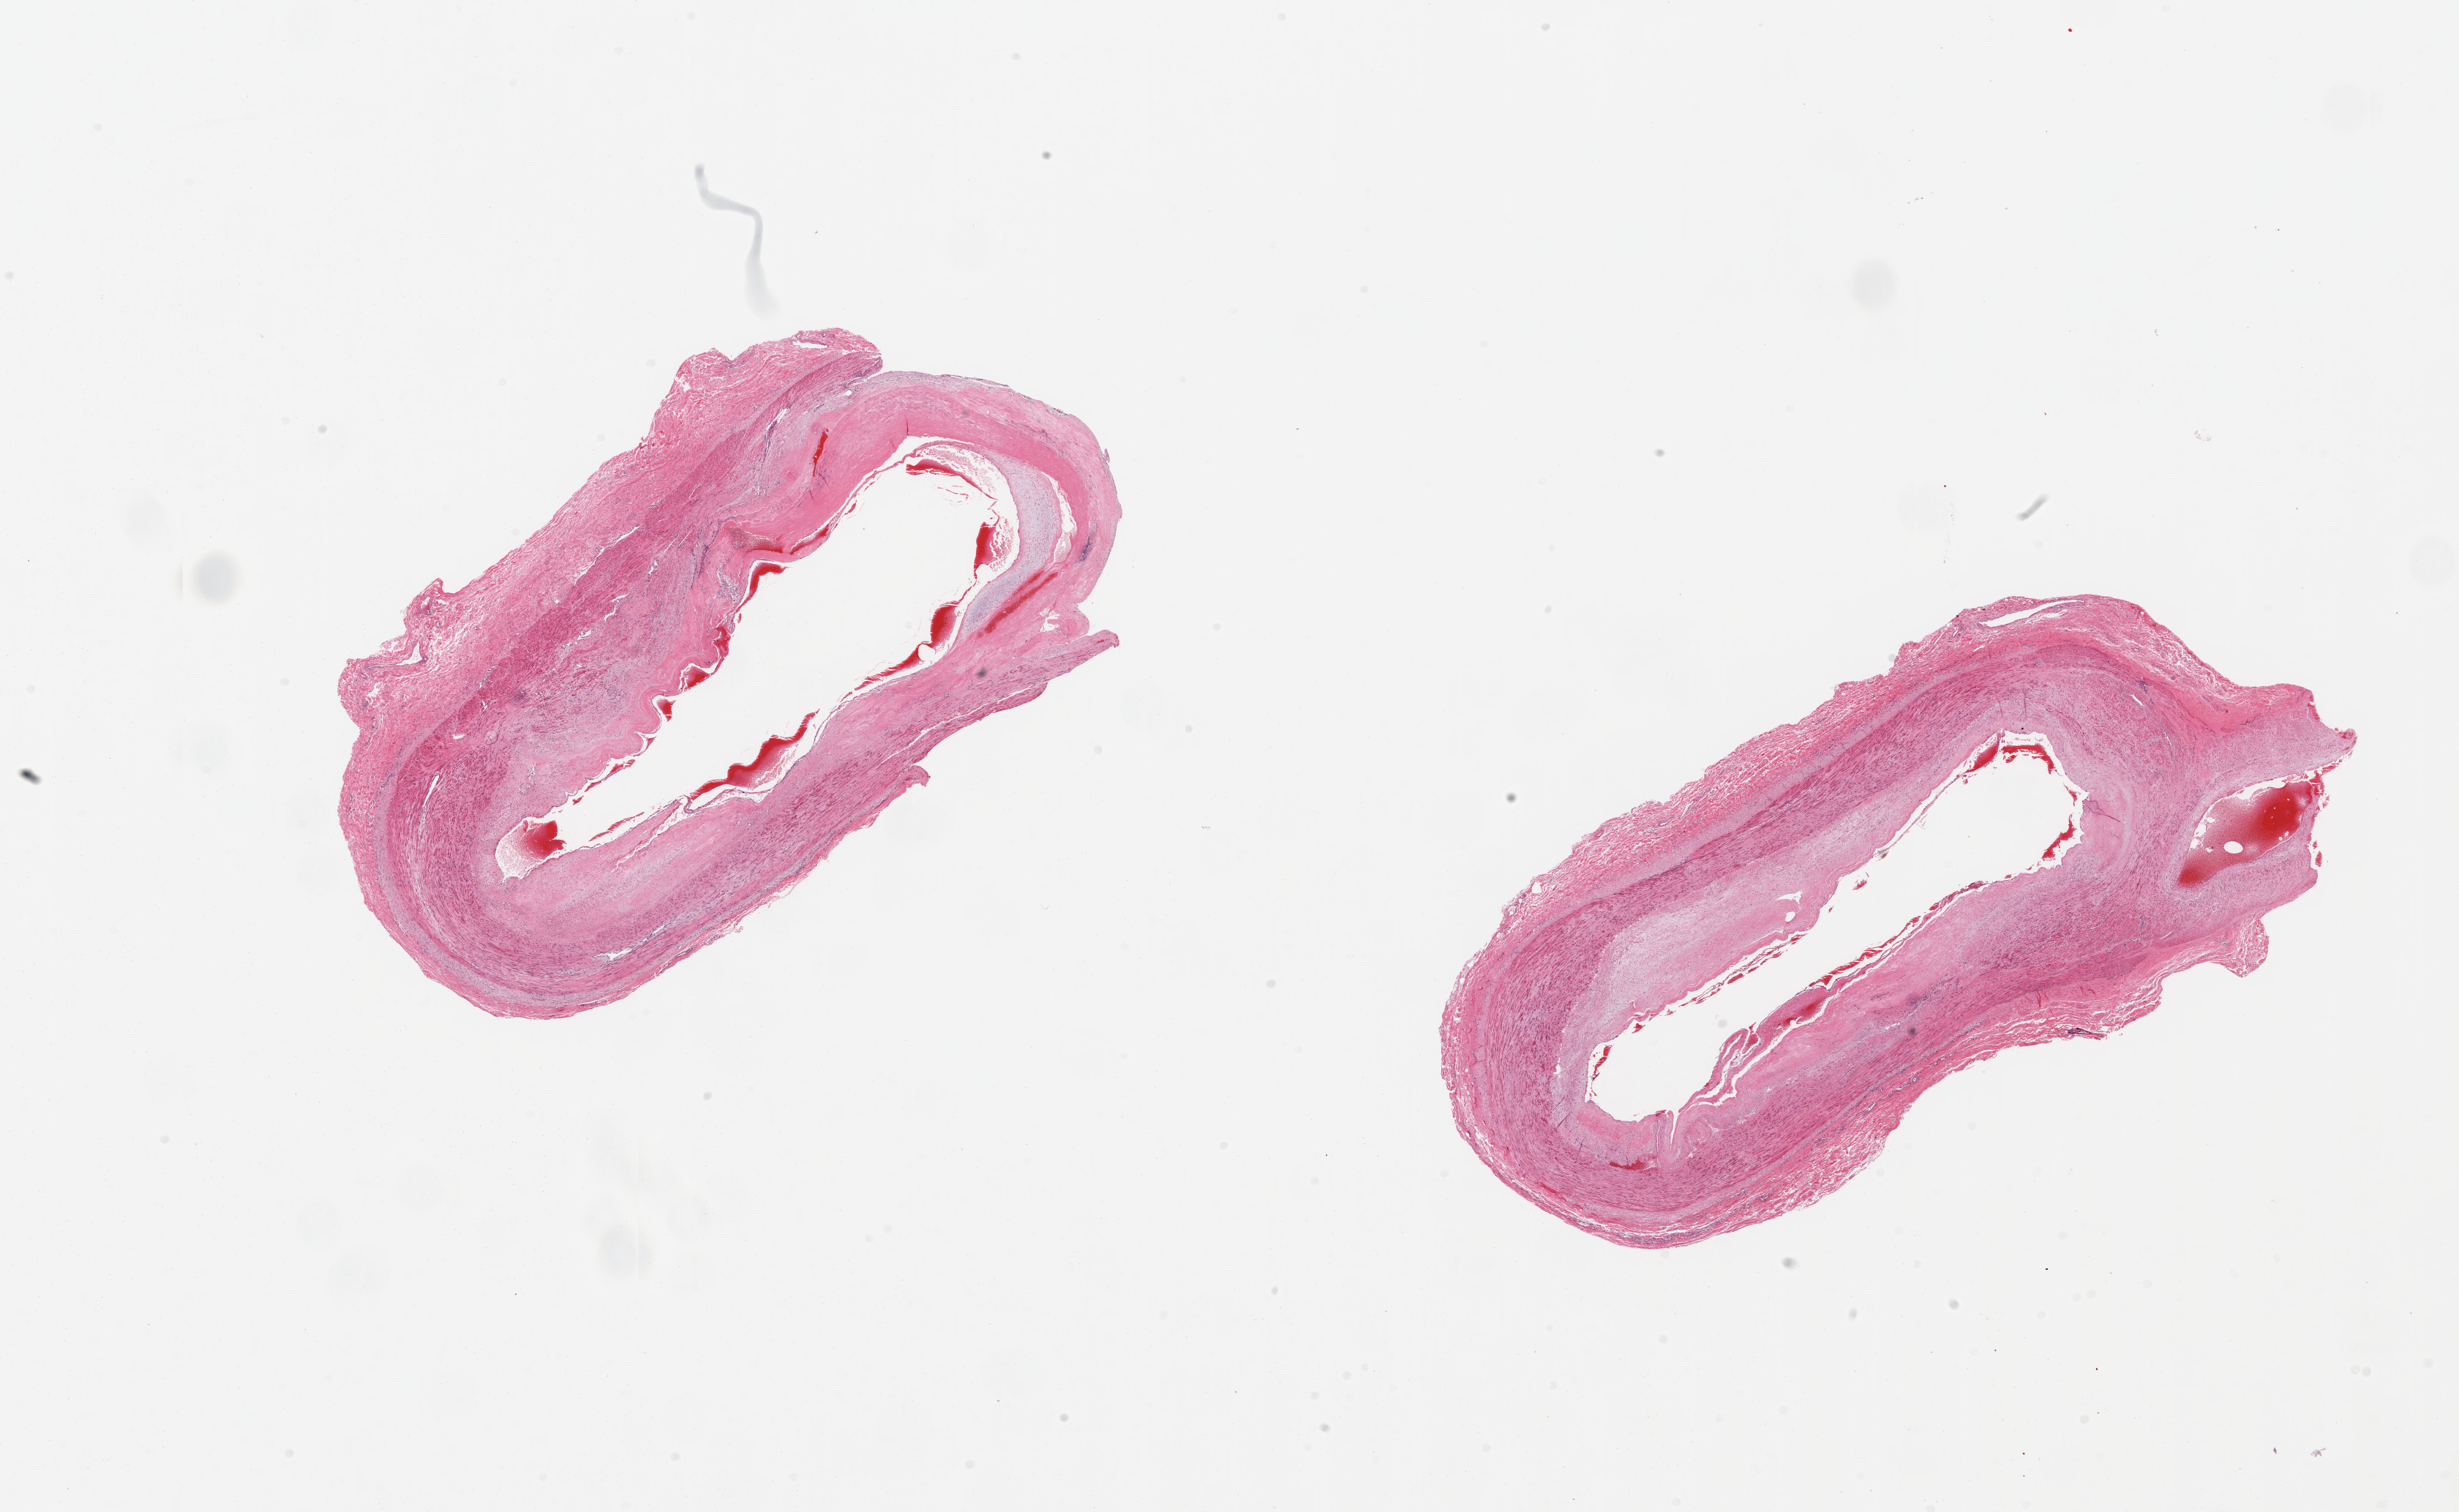
Whole-slide image, H&E stain, whole scanned area (about 26.6 x 16.3 mm, from a 20x scan) shown as a low-resolution overview, PAXgene-fixed, paraffin-embedded tissue, target tissue: tibial artery, donor tissue sample. Male donor.
Reviewer comment on this tissue sample: 2 pieces, ~50% circumferential occlusive atherosis.